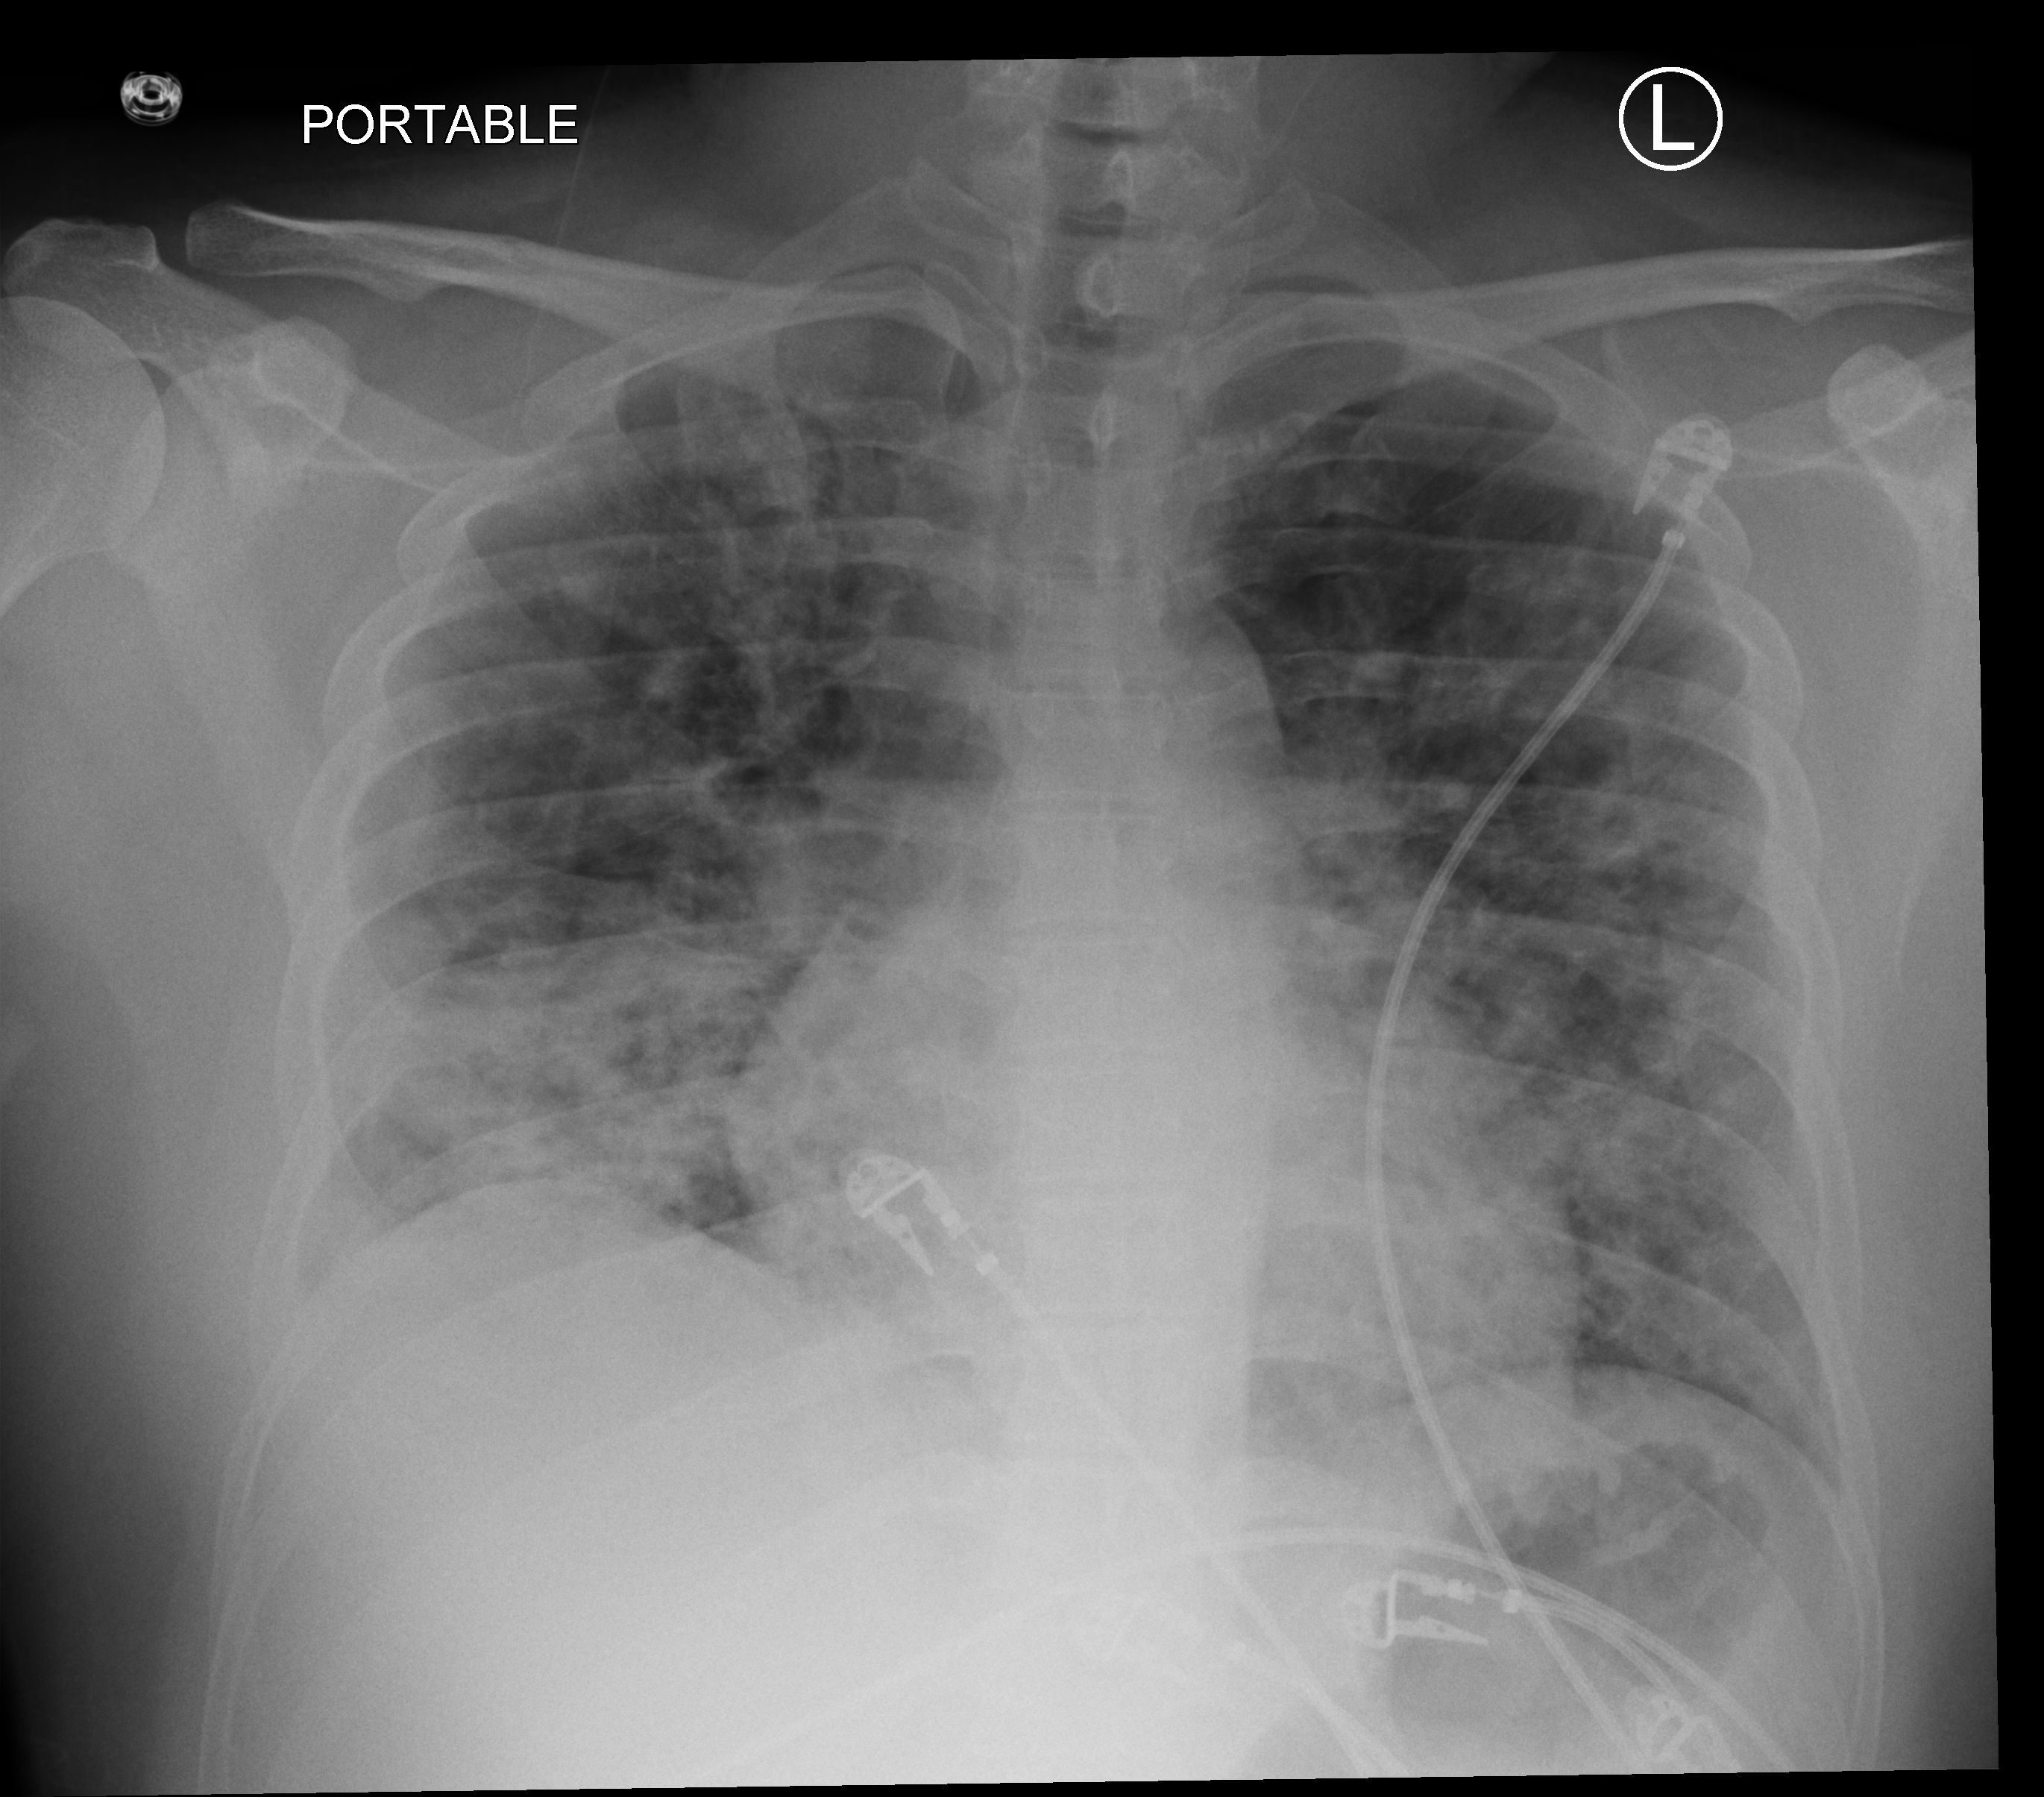
Bedside chest radiograph (computed radiography), anteroposterior (AP) projection. Patient hospitalised with COVID-19; male, aged 18–59 years.
Admission-level facts for this patient (not findings on this image; timing relative to this image not recorded): admitted to intensive care during this hospital stay: no; mechanically ventilated during this hospital stay: no.